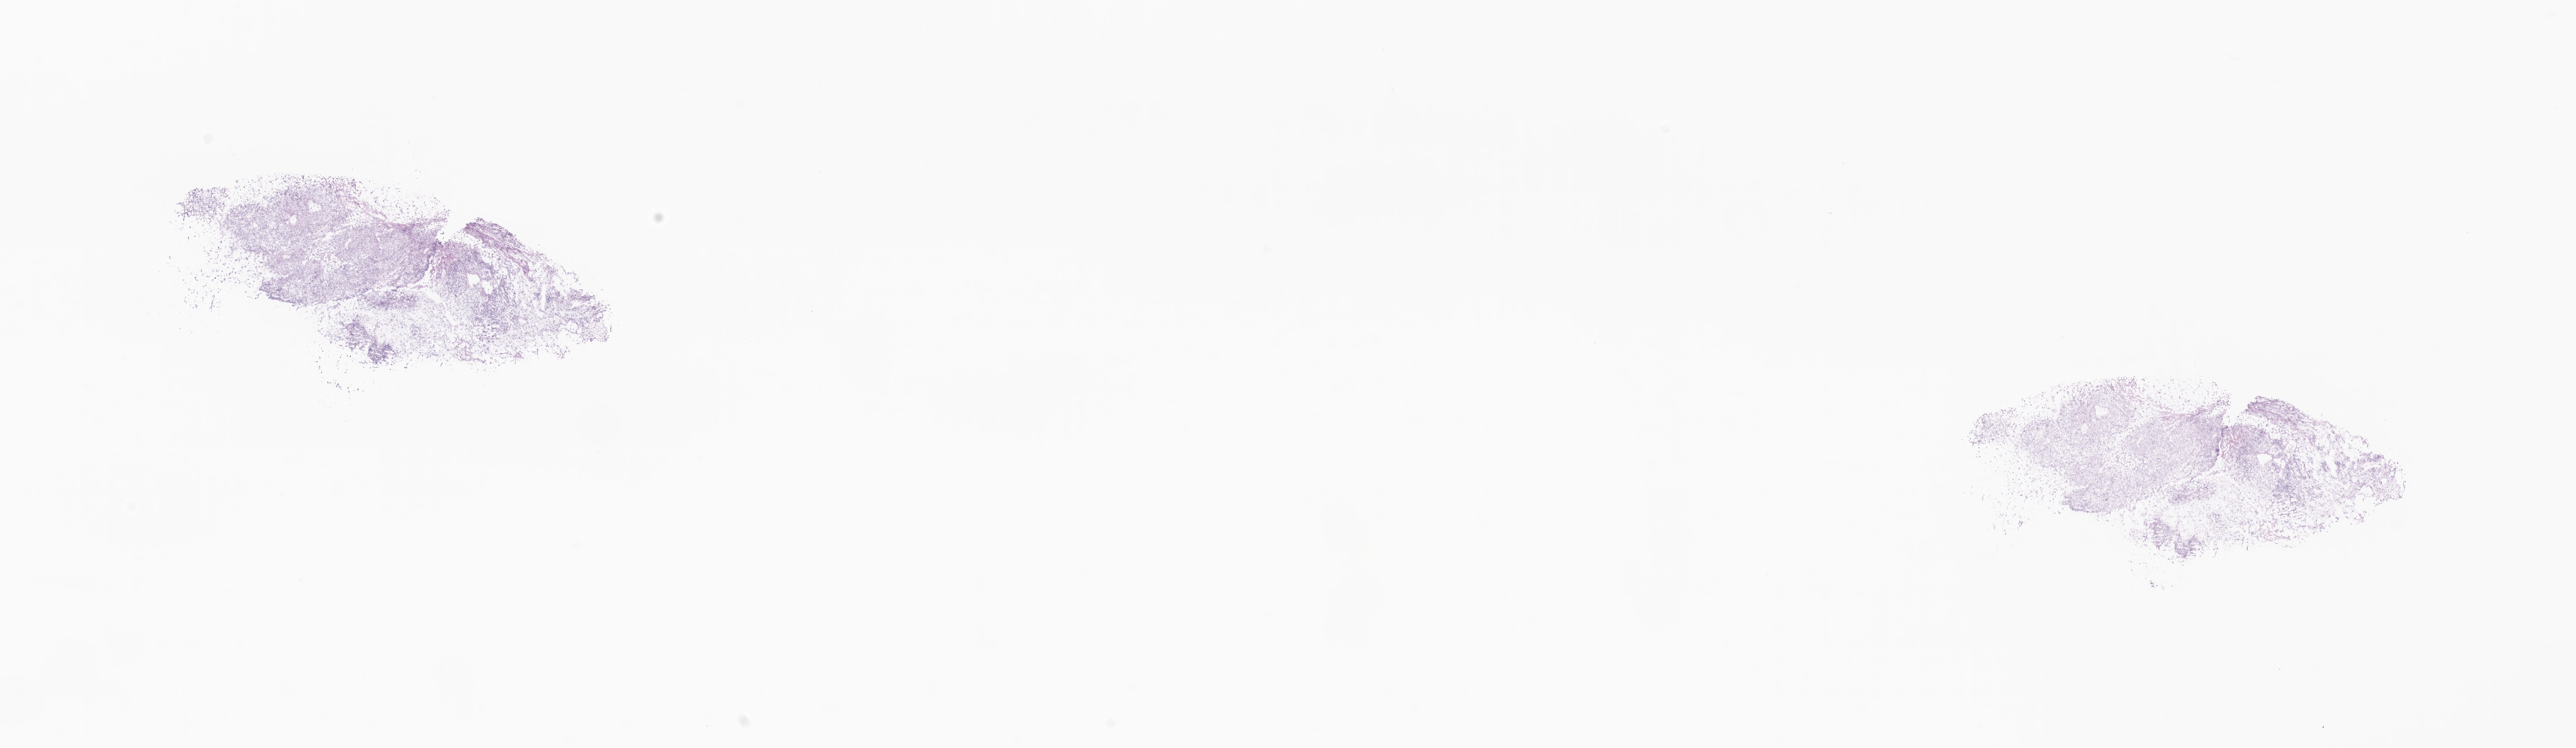
Whole-slide image, hematoxylin and eosin (H&E) stain, a low-resolution overview of the entire scanned area, about 27.3 x 7.9 mm. Frozen section. Specimen: primary tumor. Site: lung. Patient: female, age at initial diagnosis 49 years. Slide review estimates, as recorded: tumor cells 95%, tumor nuclei 95%, stromal cells 5%, necrosis 0%, normal cells 0%. Infiltration values recorded for this section: lymphocyte infiltration 1%, monocyte infiltration 0%, neutrophil infiltration 1%.
- diagnosis: Leiomyosarcoma, NOS